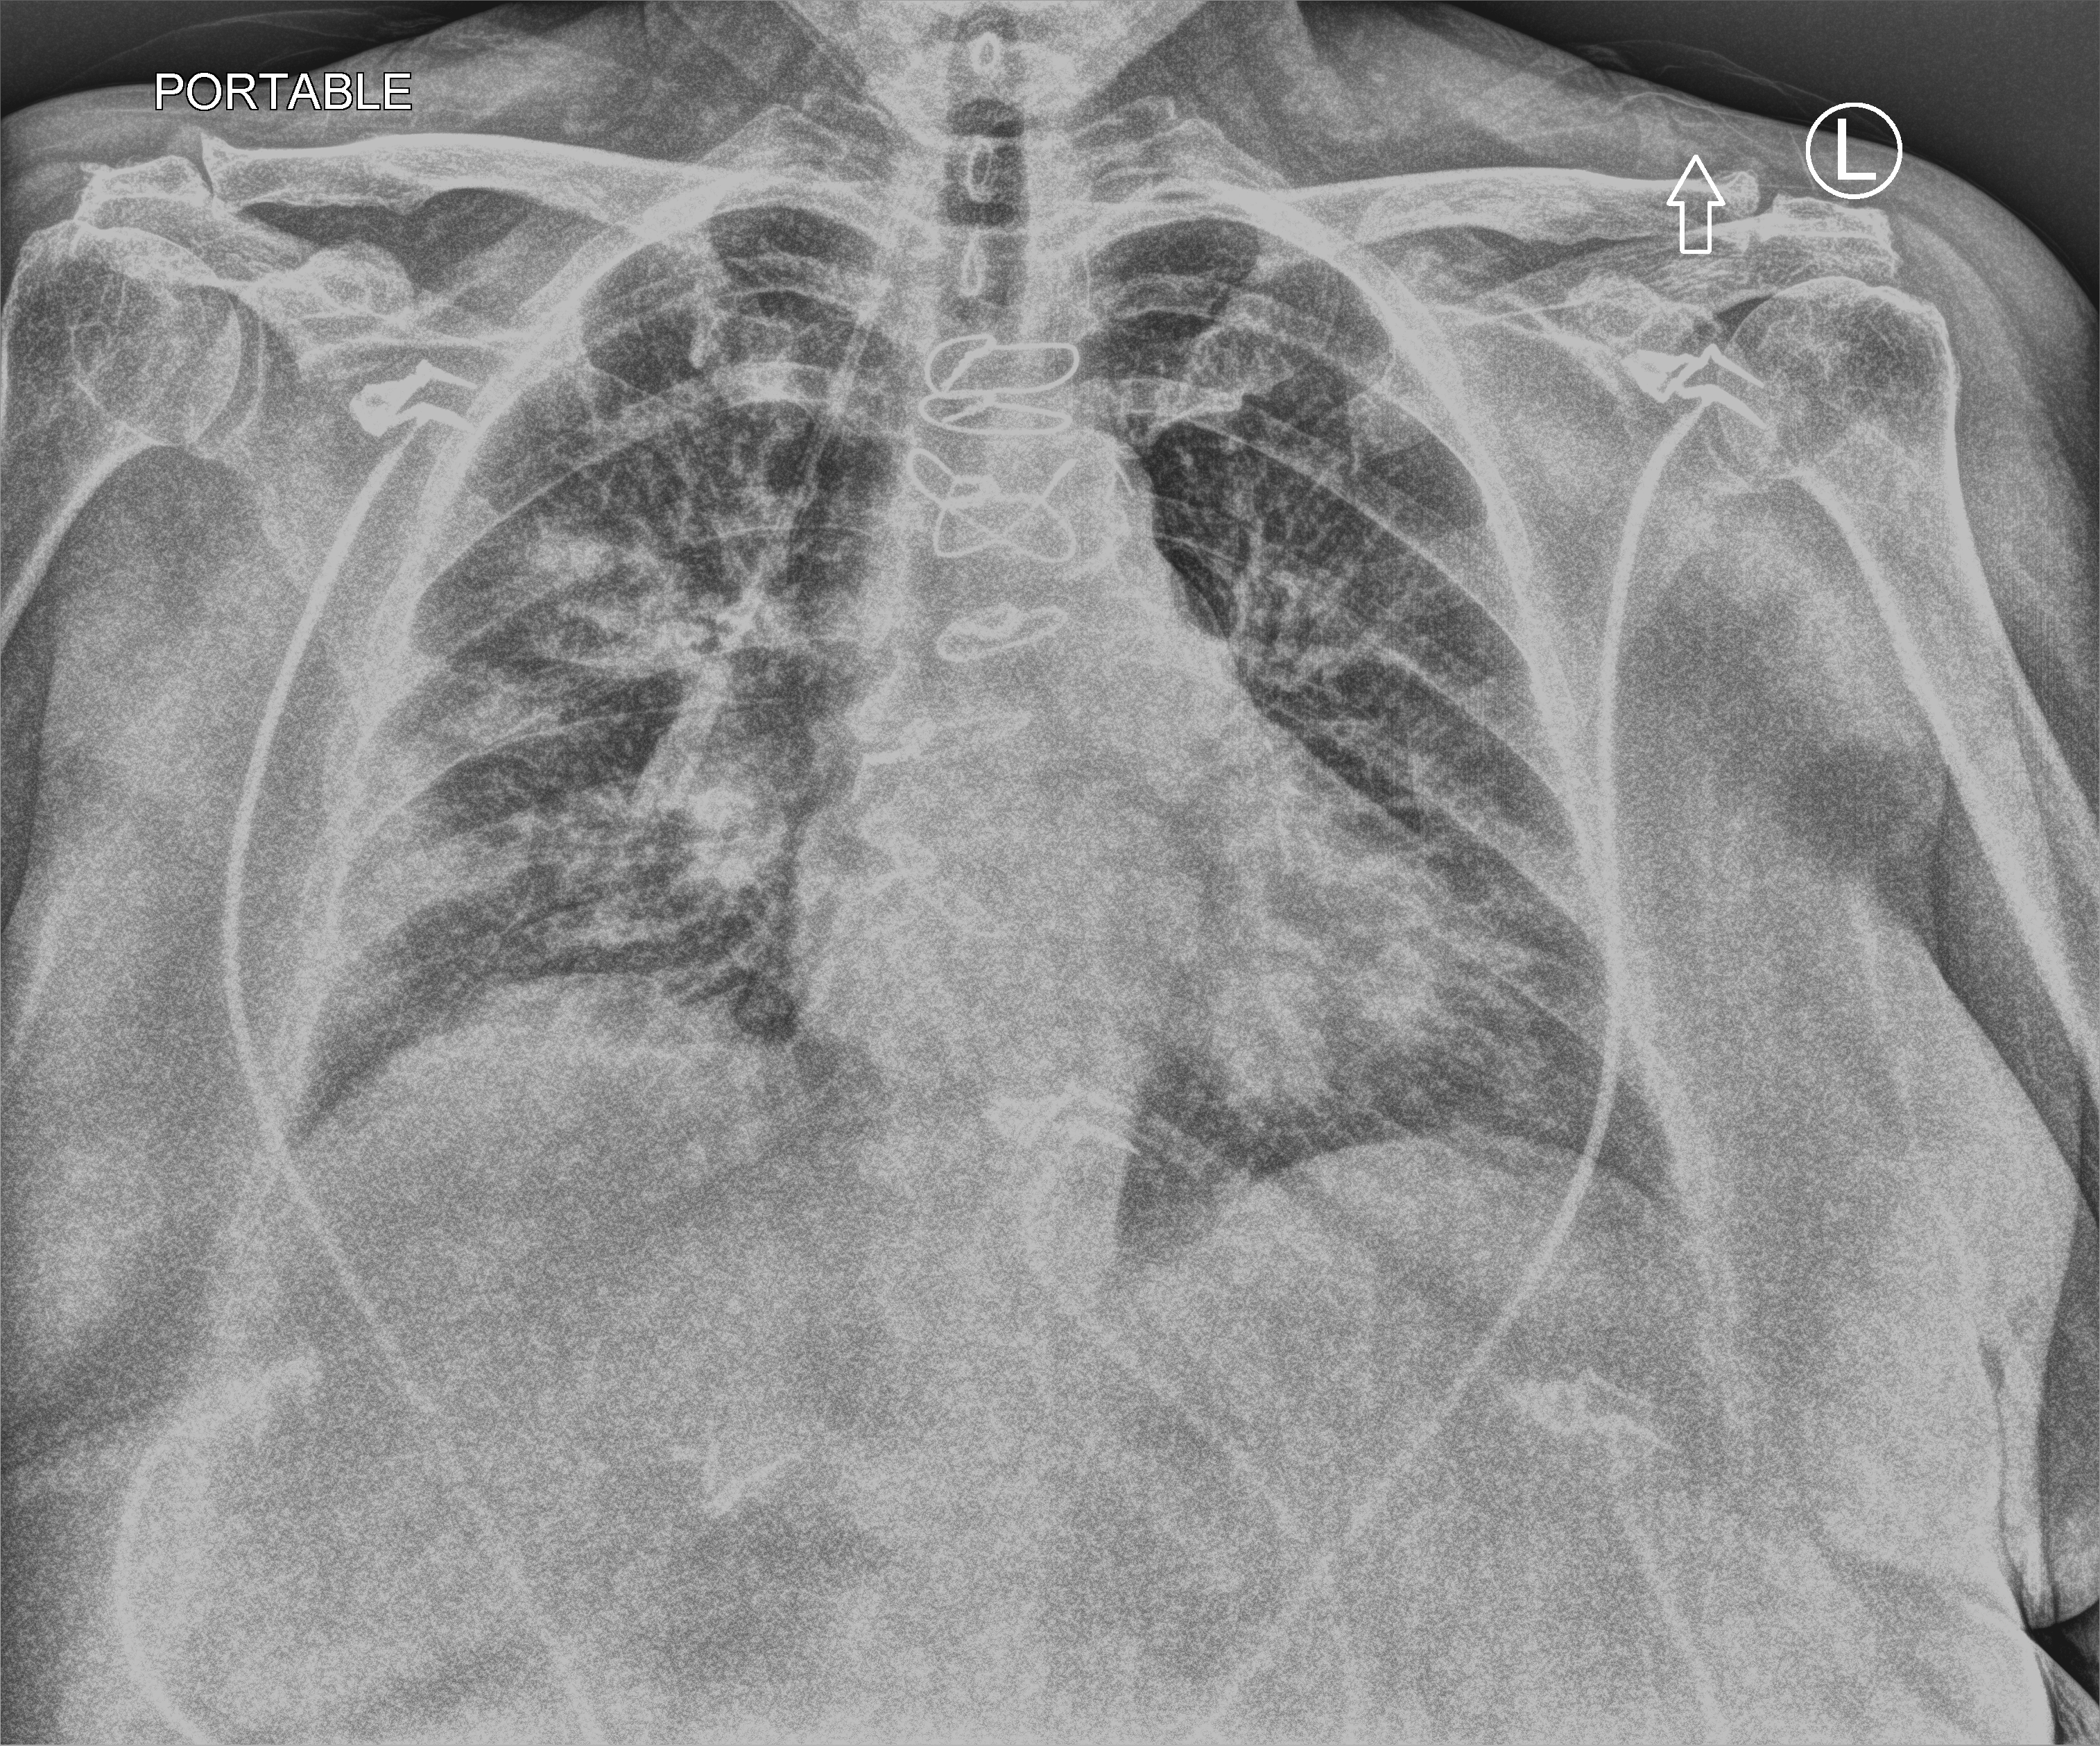
Chest X-ray (portable), anteroposterior (AP) projection. Female patient hospitalised with COVID-19, age 60–74 years.
Admission-level facts for this patient (not findings on this image; timing relative to this image not recorded): admitted to intensive care during this hospital stay: no; length of hospital stay: 13 days; mechanically ventilated during this hospital stay: no.